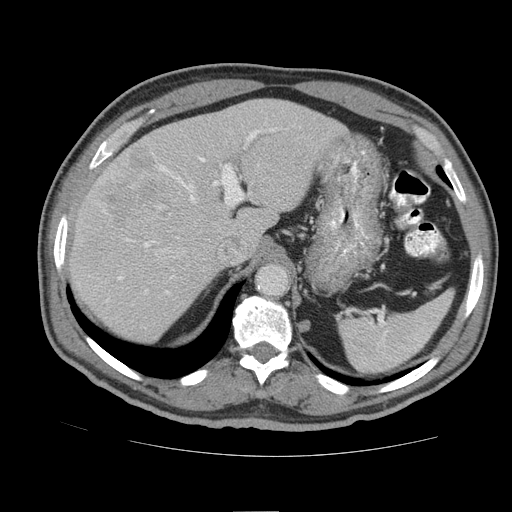
Contrast-enhanced abdominal CT (liver protocol), one axial slice; position 63 of 105 along the scan axis; reconstruction kernel STANDARD; soft-tissue window (W 400 / L 40 HU); 512 × 512 image matrix, field of view 380 × 380 mm. Case-level facts recorded for this patient, not image findings: diagnosis: hepatocellular carcinoma (patient treated with transarterial chemoembolisation; whether this scan precedes or follows treatment is not stated here); TNM stage (as recorded): Stage-IIIB; Child-Pugh class: A.
Structures marked on this image (semi-automatically segmented with operator editing):
- liver parenchyma outside the tumour (the mass and vessels are separate outlines, so this box may not span the whole liver): bounding box (x1, y1, x2, y2) in pixels: (68, 98, 352, 342)
- mass: (100, 144, 166, 234)
- liver vessels: (103, 129, 275, 294)